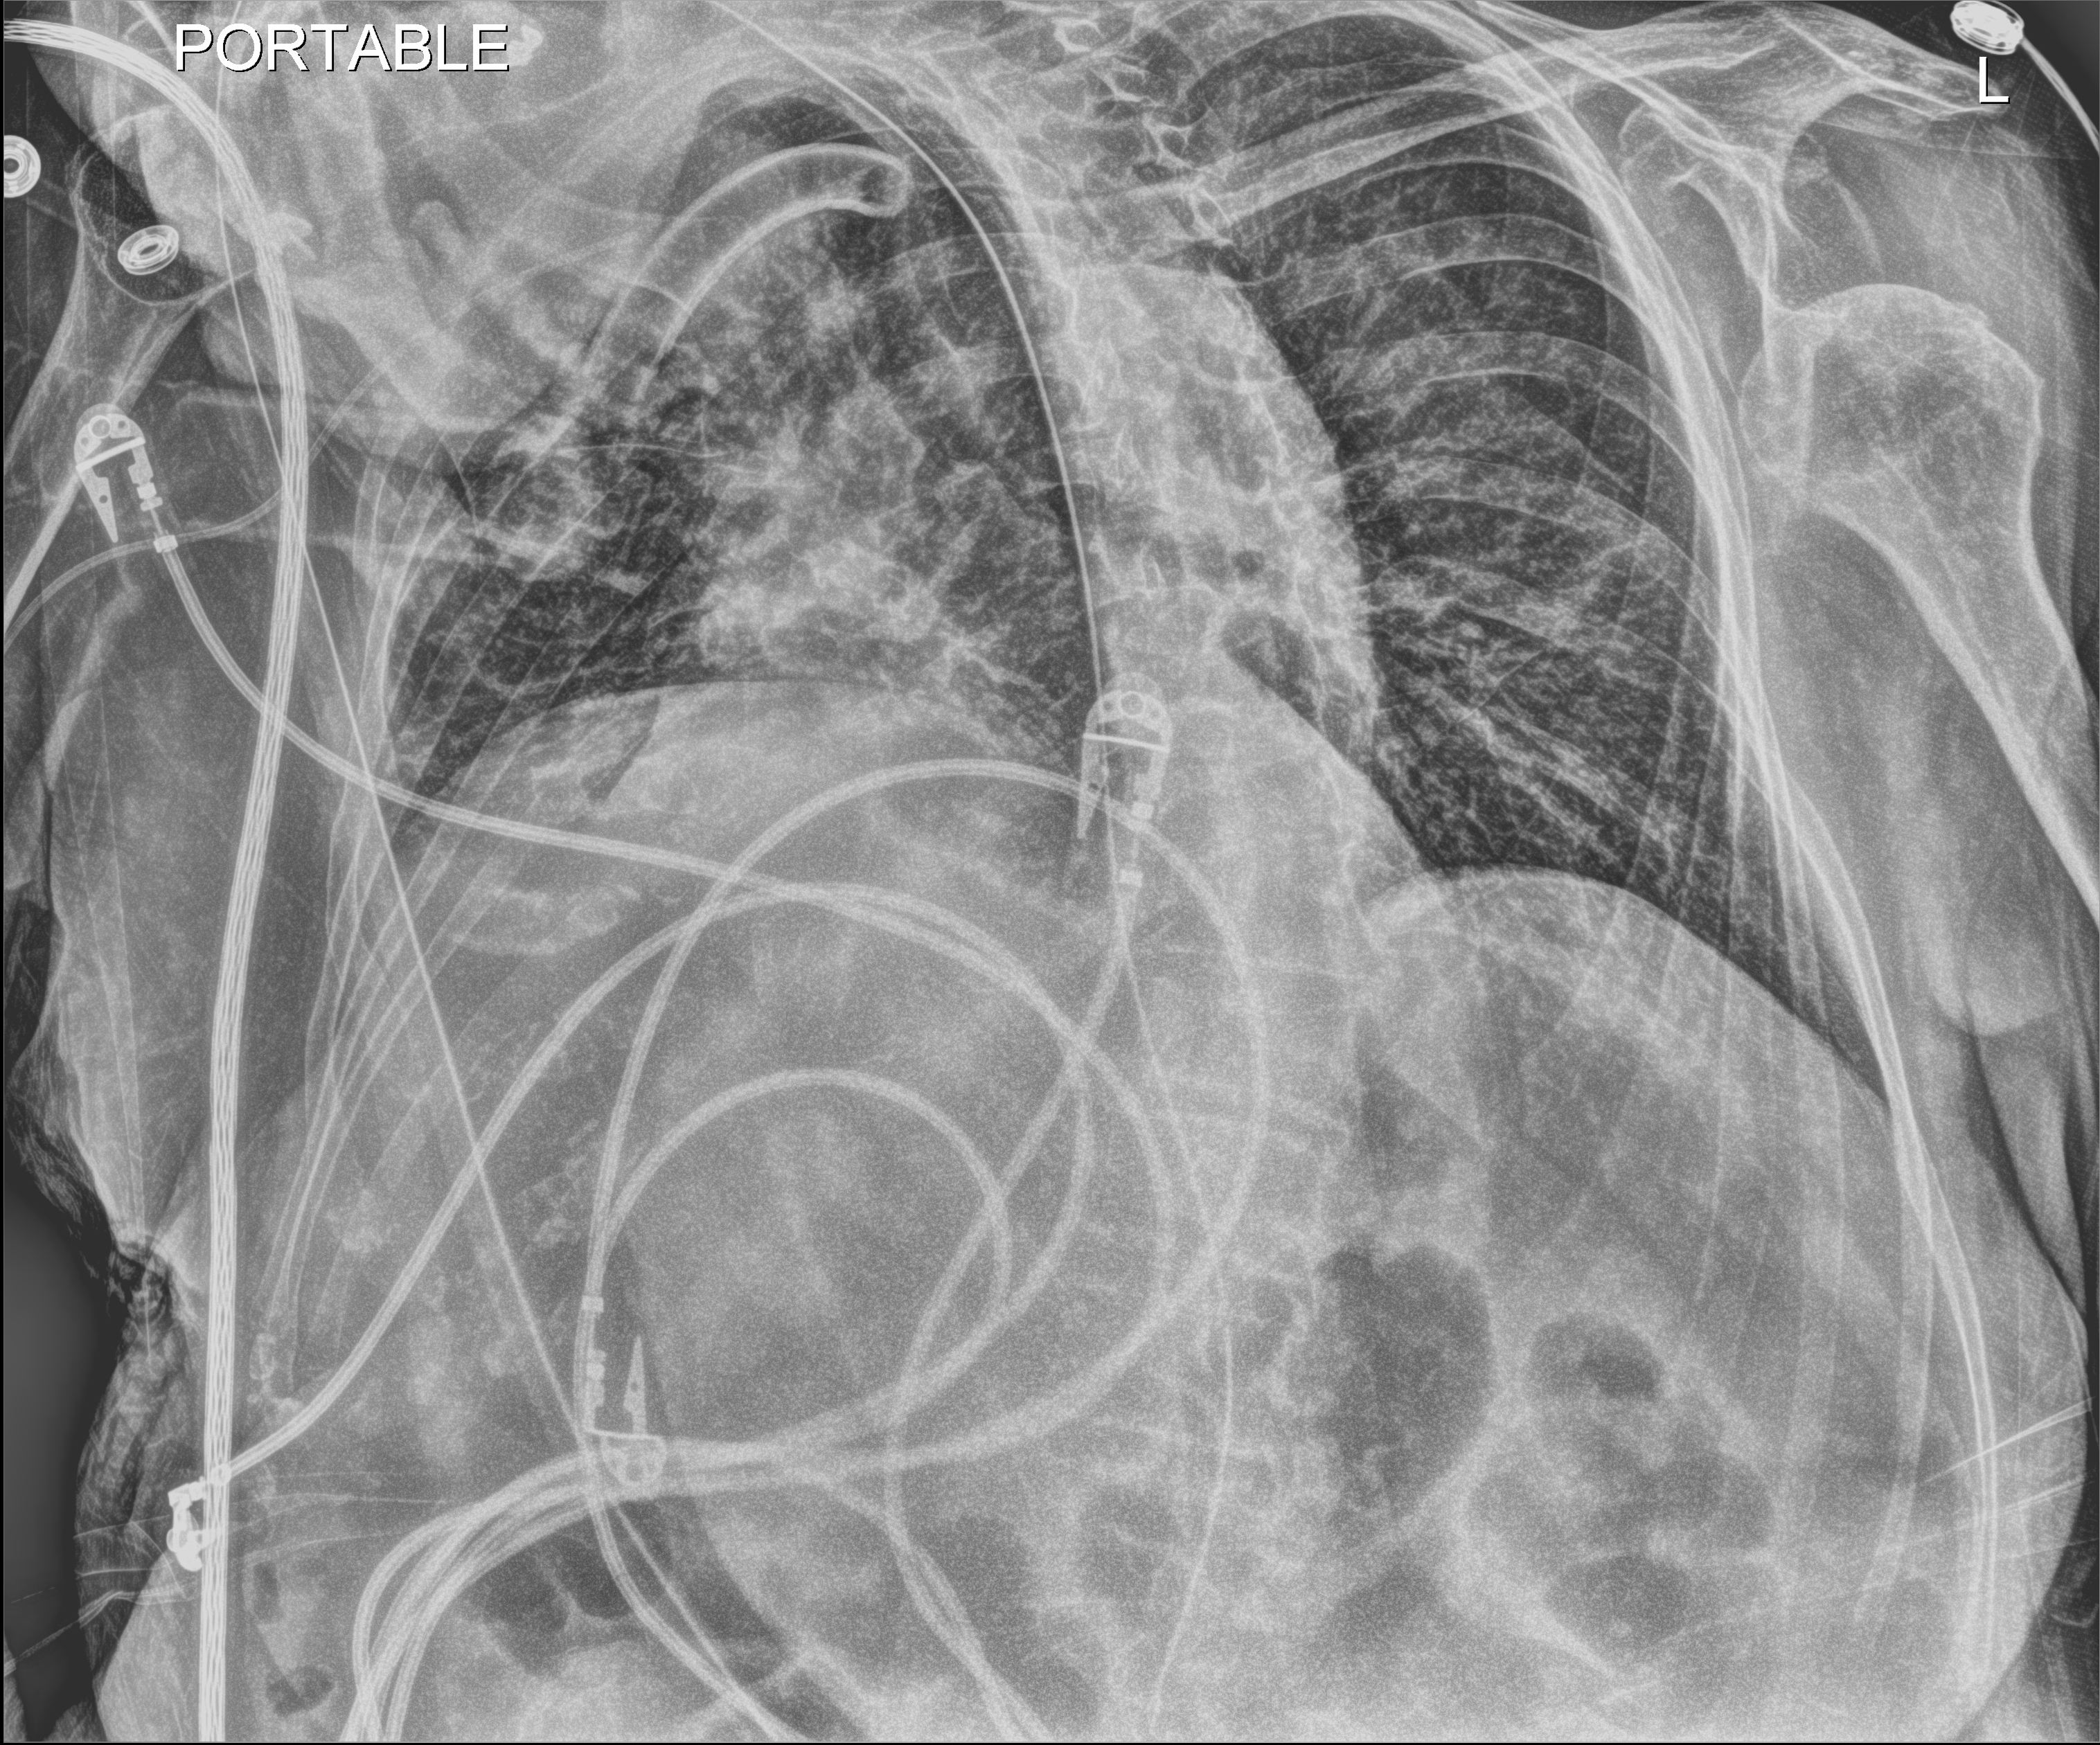
Chest X-ray; anteroposterior (AP) projection. Patient hospitalised with COVID-19; female, aged 75–90 years.
From the hospital-stay record, not from the radiograph (when in the stay this image was taken is not recorded): mechanically ventilated during this hospital stay: yes; admitted to intensive care during this hospital stay: yes.